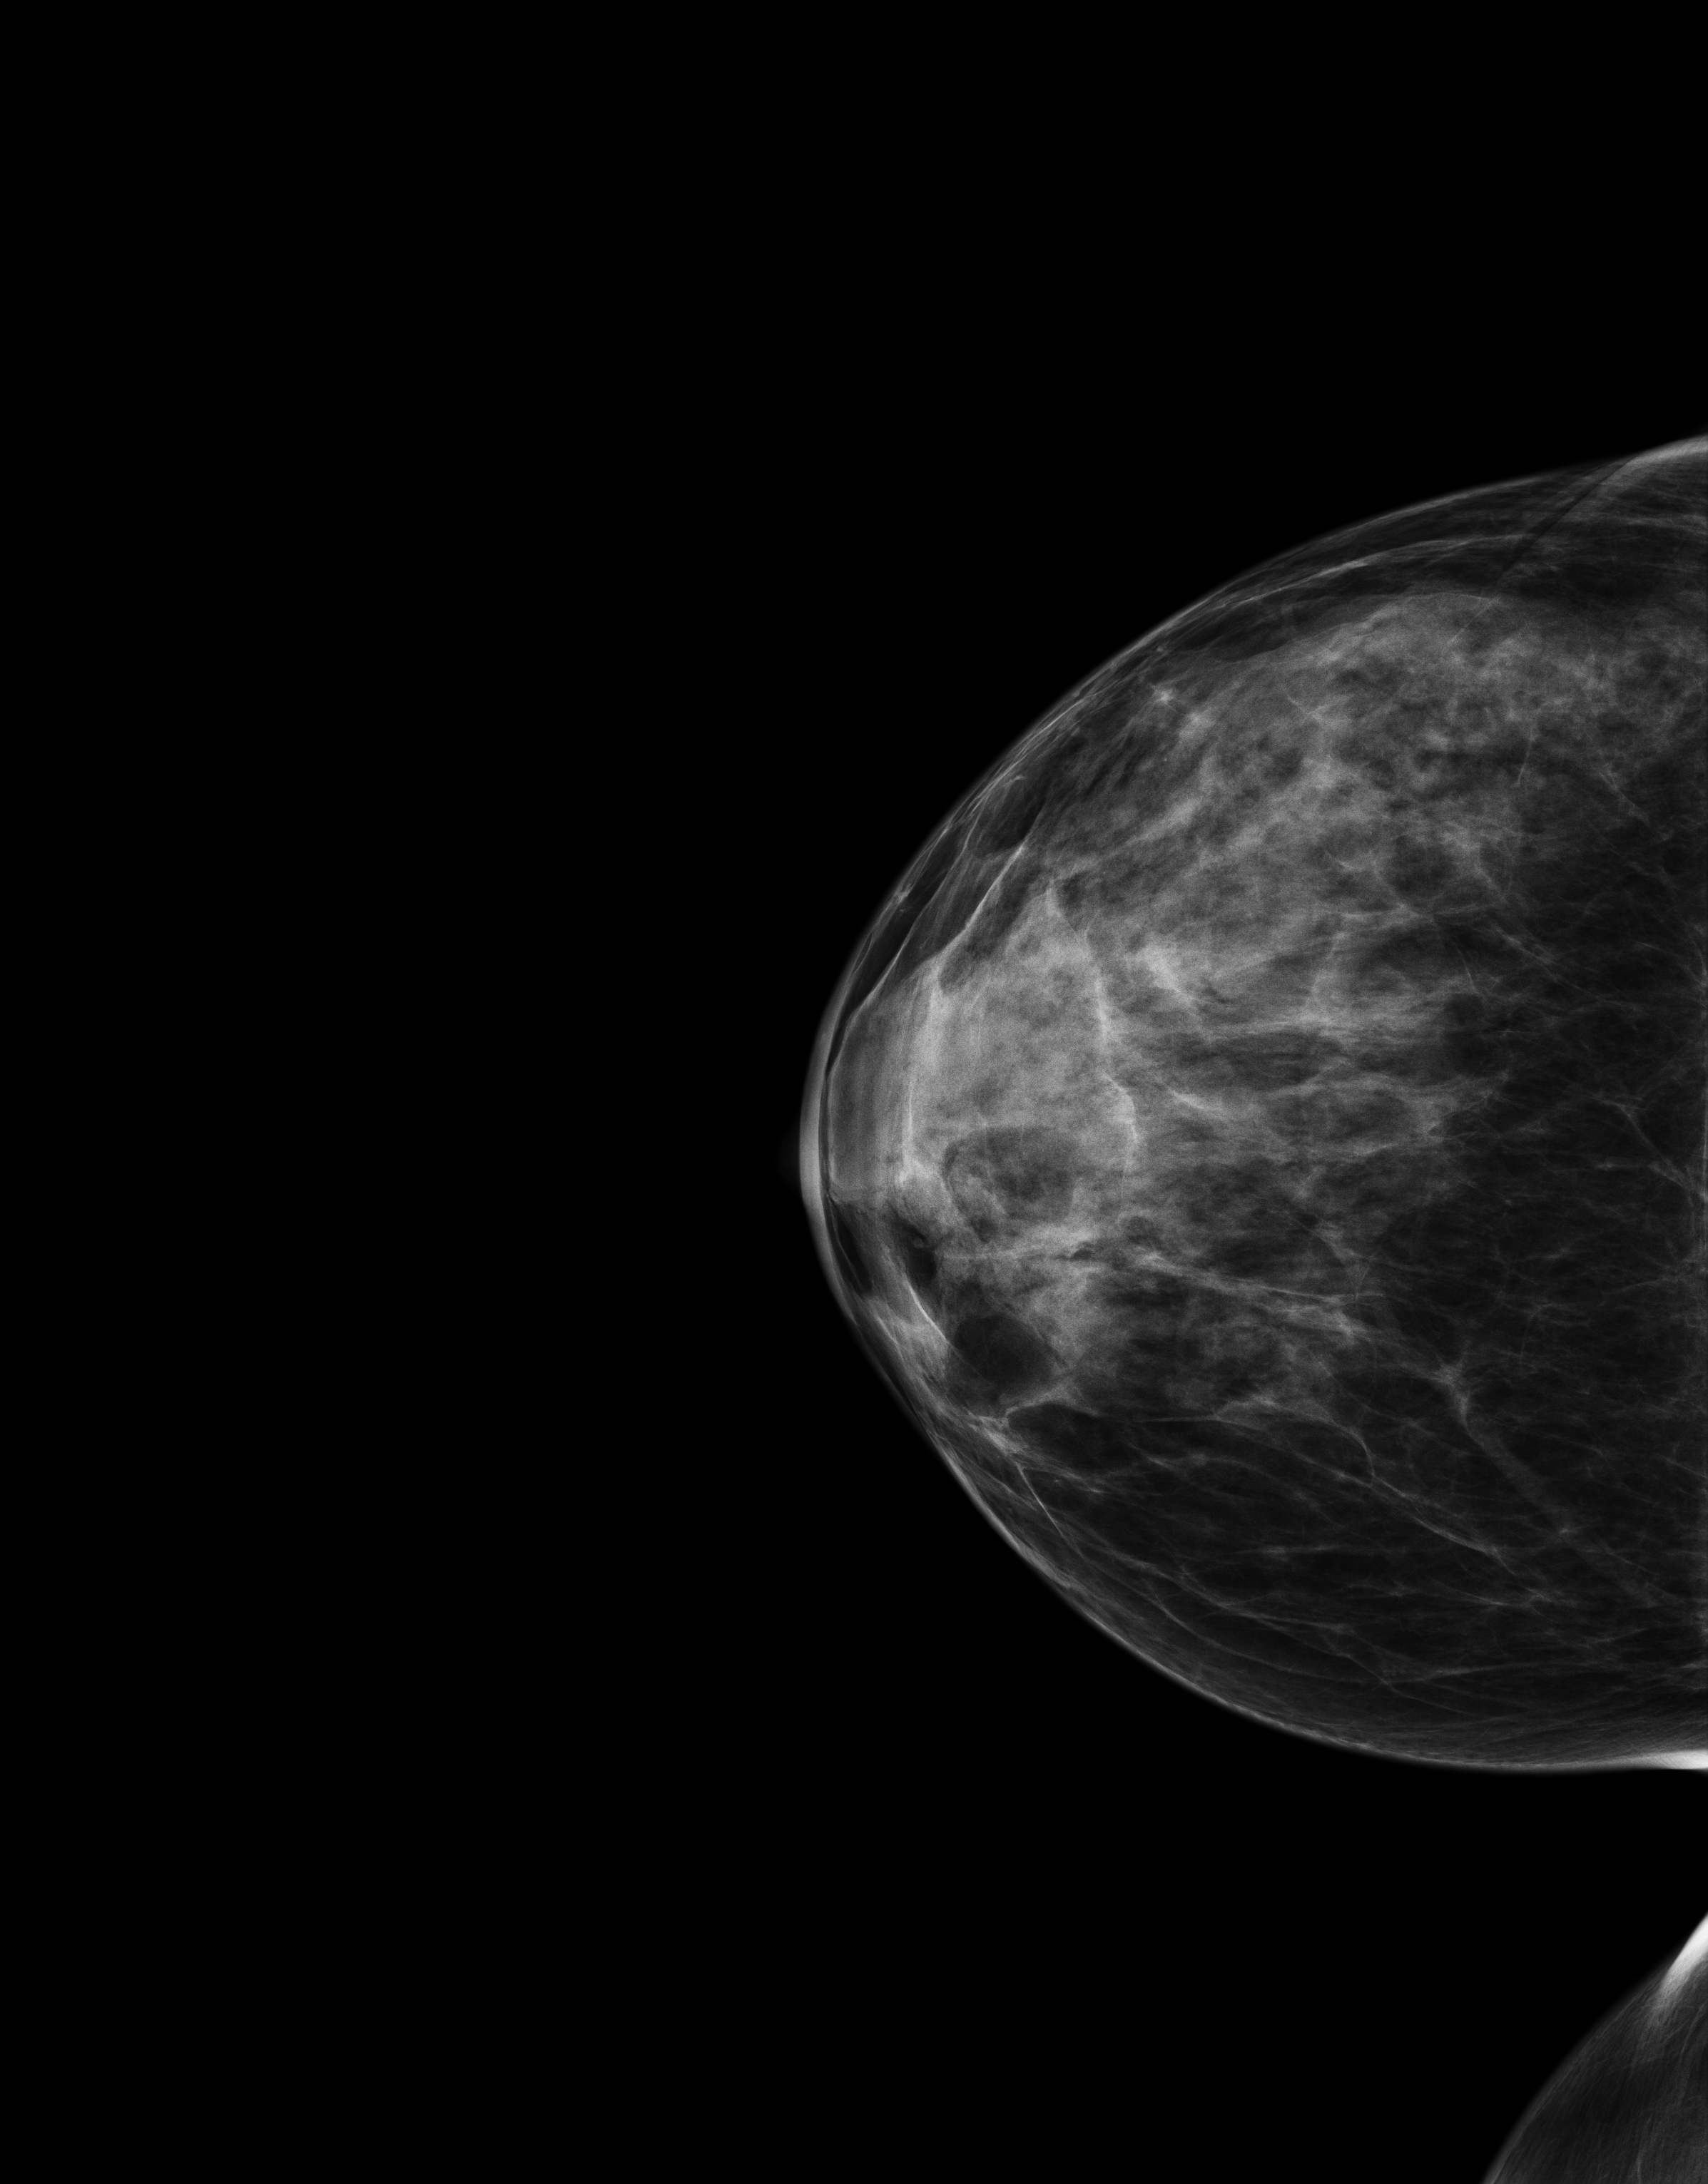
Screening examination; compressed breast thickness 46 mm. Patient aged 49 years (female).
Image type: full-field digital mammogram. Breast: right. Projection: craniocaudal (CC) view.